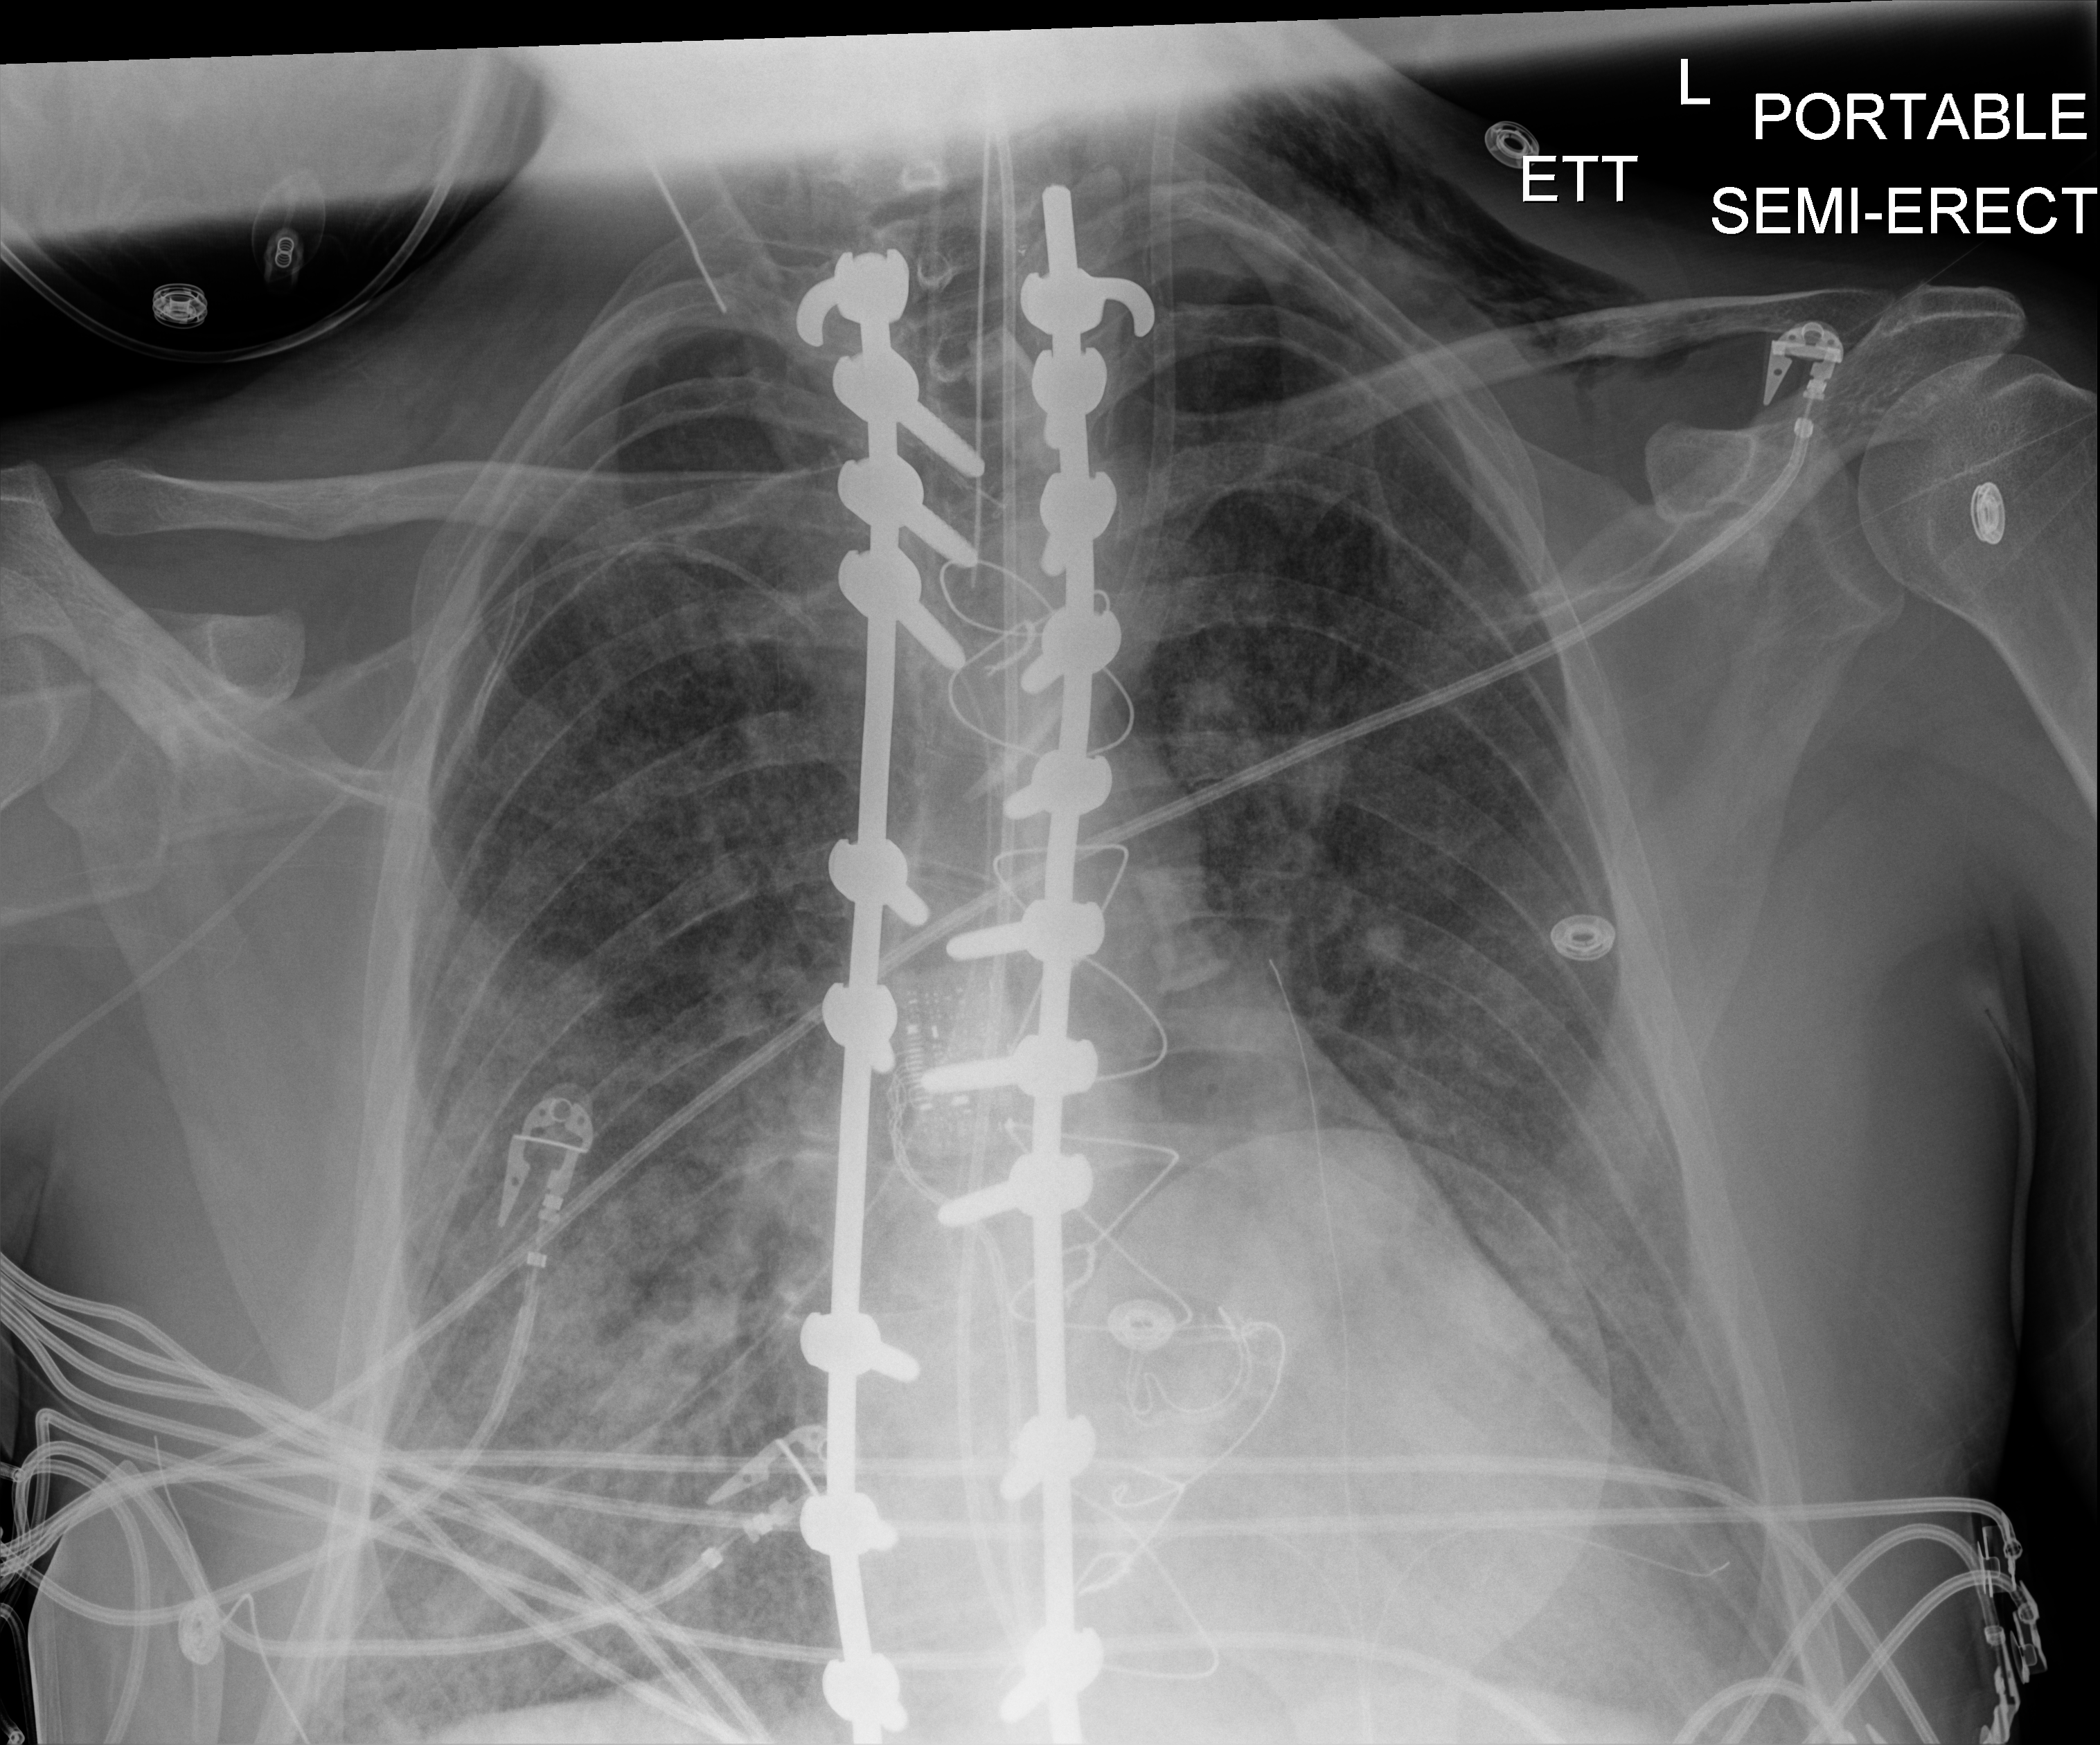
Portable chest radiograph; anteroposterior (AP) projection. Patient hospitalised with COVID-19, aged 18–59 years.
Hospital-stay facts (about this admission, not read from this image; timing relative to this image not recorded):
- mechanically ventilated during this hospital stay: yes
- length of hospital stay: 15 days
- admitted to intensive care during this hospital stay: yes